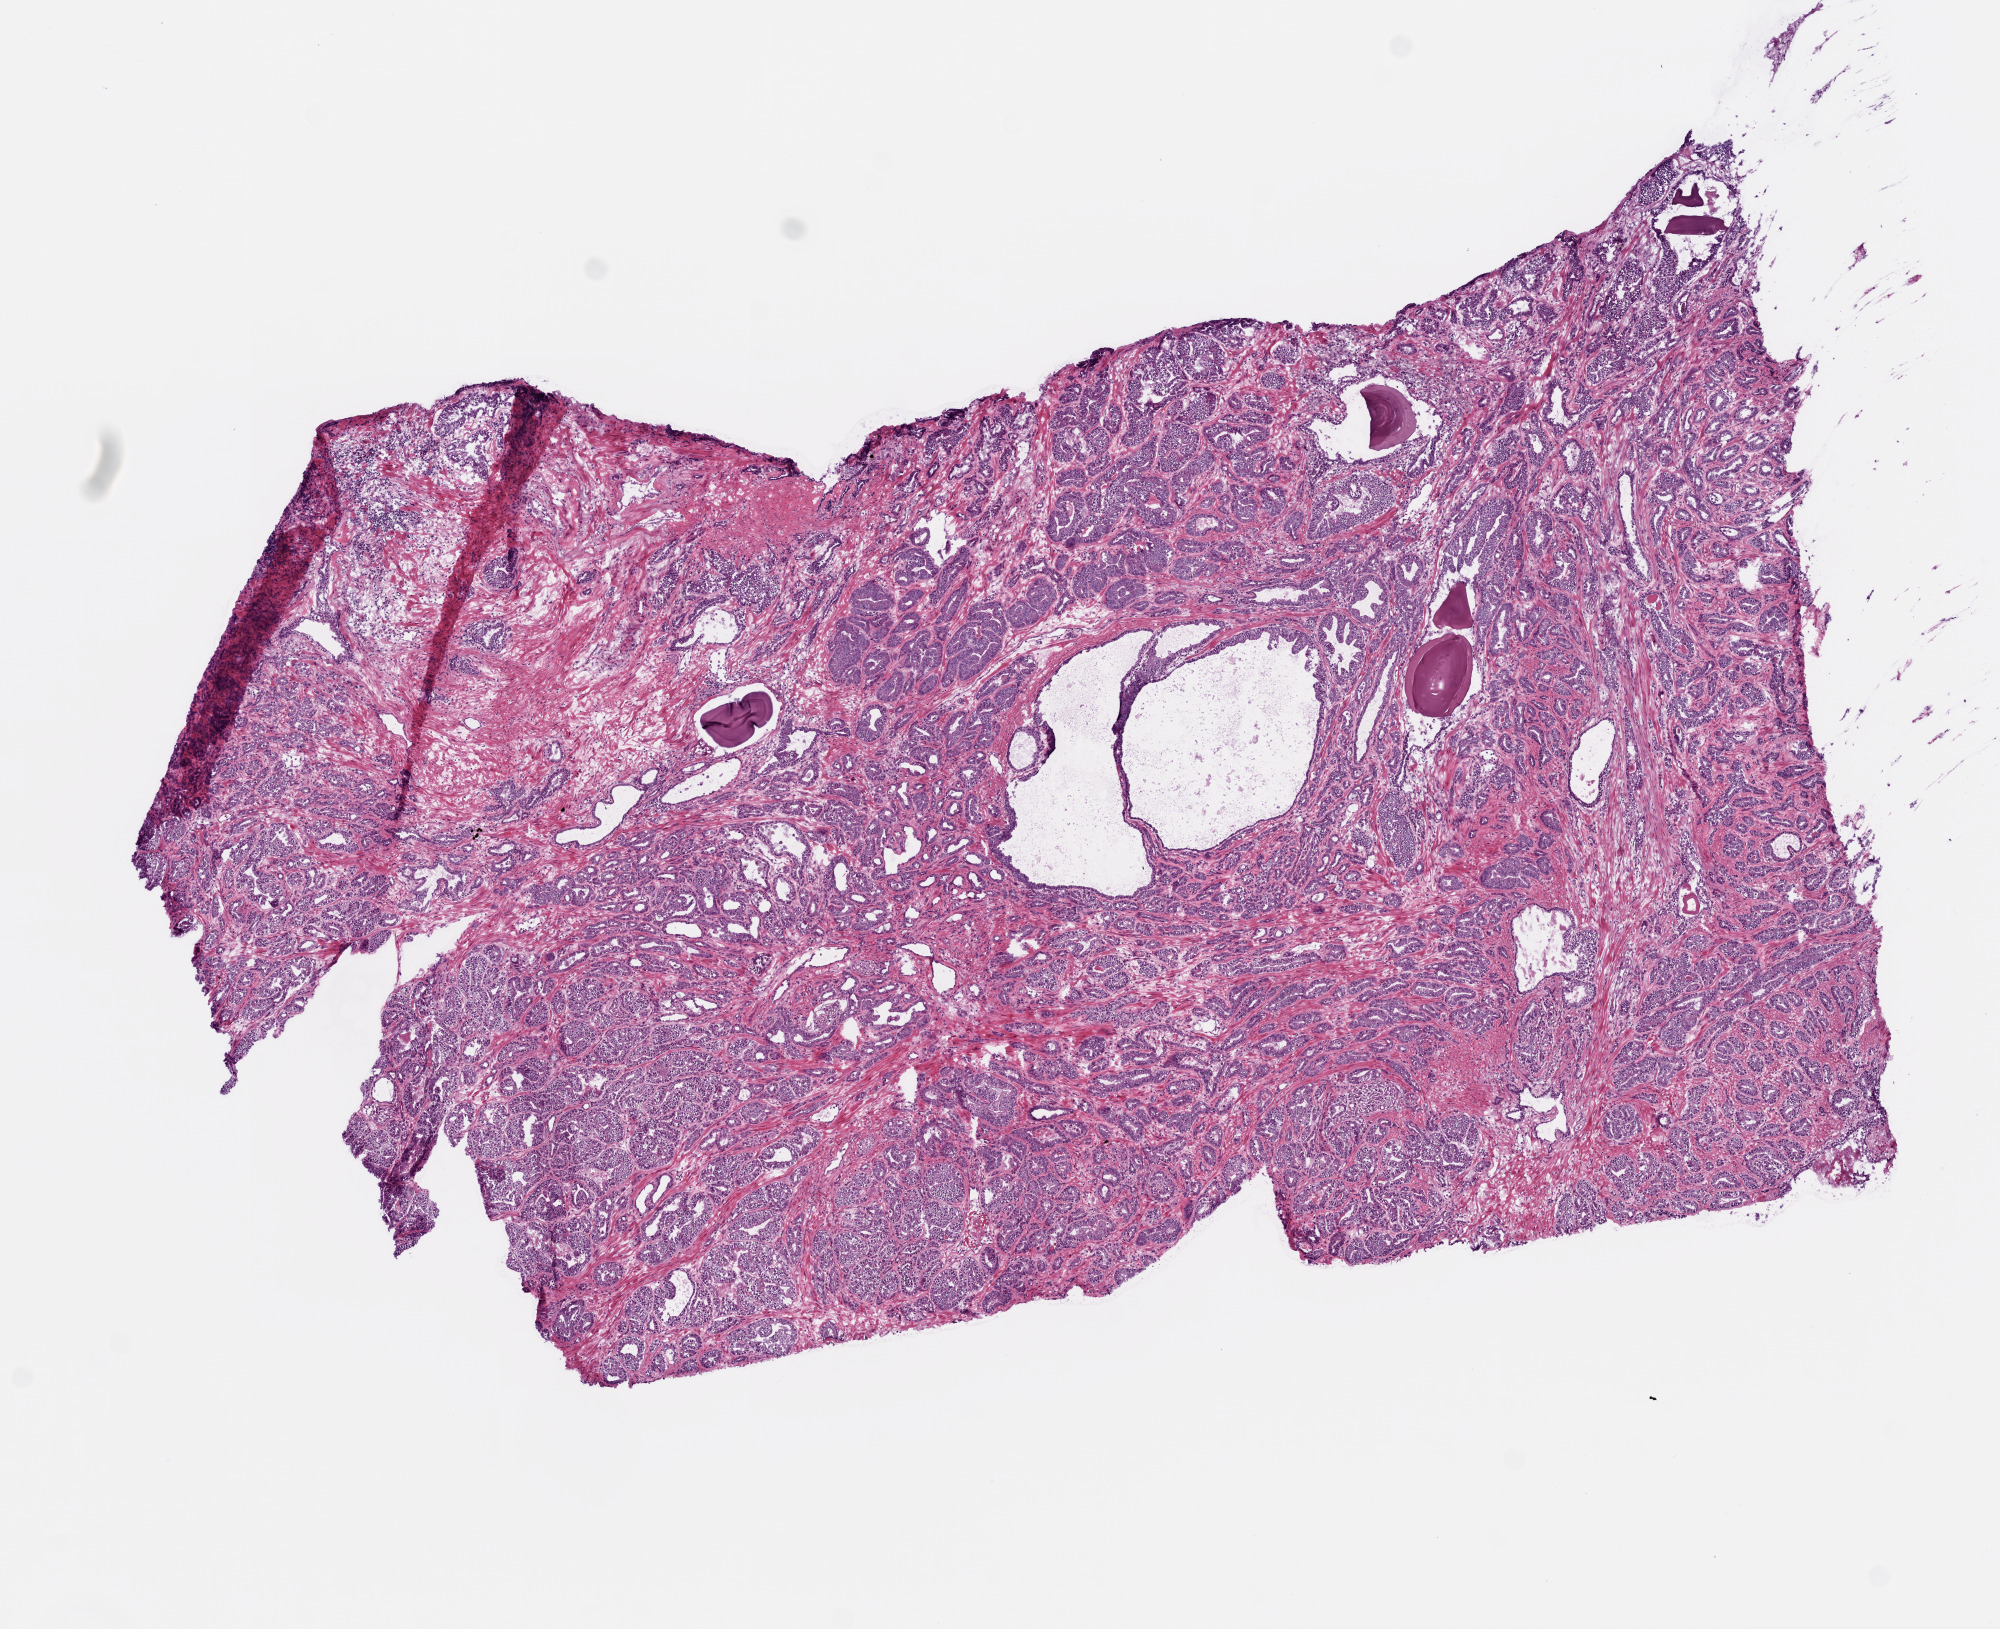
Digitized Hematoxylin and eosin (H&E) stained tissue section (whole slide), a low-resolution overview of the entire scanned area, about 8.0 x 6.5 mm, frozen section, sample: primary tumour, prostate. Male patient; age at initial diagnosis 66 years. Gleason score: 7 (3+4). Composition of this section per pathologist review: tumour cells 65%, tumour nuclei 70%, normal cells 20%, stromal cells 15%, necrosis 0%. Inflammatory infiltration, as recorded: lymphocyte infiltration 0%, monocyte infiltration 0%, neutrophil infiltration 0%.
- diagnosis: Acinar cell carcinoma (prostate gland)
- laterality: bilateral